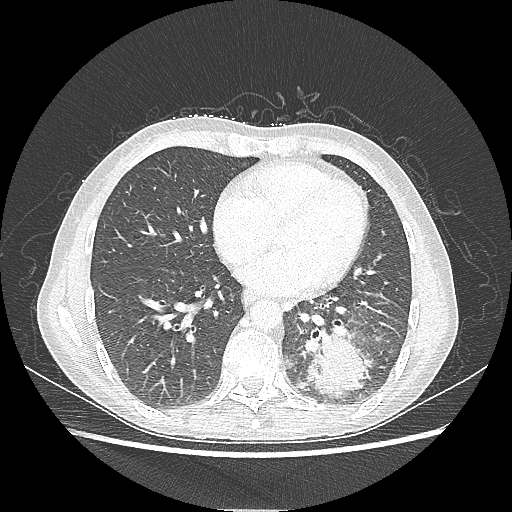
Chest CT, one axial slice. Slice 88 of 220 in the series (ordered by position). 80 kVp. Lung window (W 1500 / L -600 HU). 1.25 mm slice thickness. 512 × 512 image matrix, field of view 360 × 360 mm. Female patient, age 53 years. From the clinical record (not read from this slice): clinical TNM (as recorded): T3 N0 M0.
Annotated regions visible in this slice (bounding box drawn by a radiologist):
- lung tumour (recorded histology: adenocarcinoma): bounding box [x1, y1, x2, y2] px = [305, 328, 376, 400]